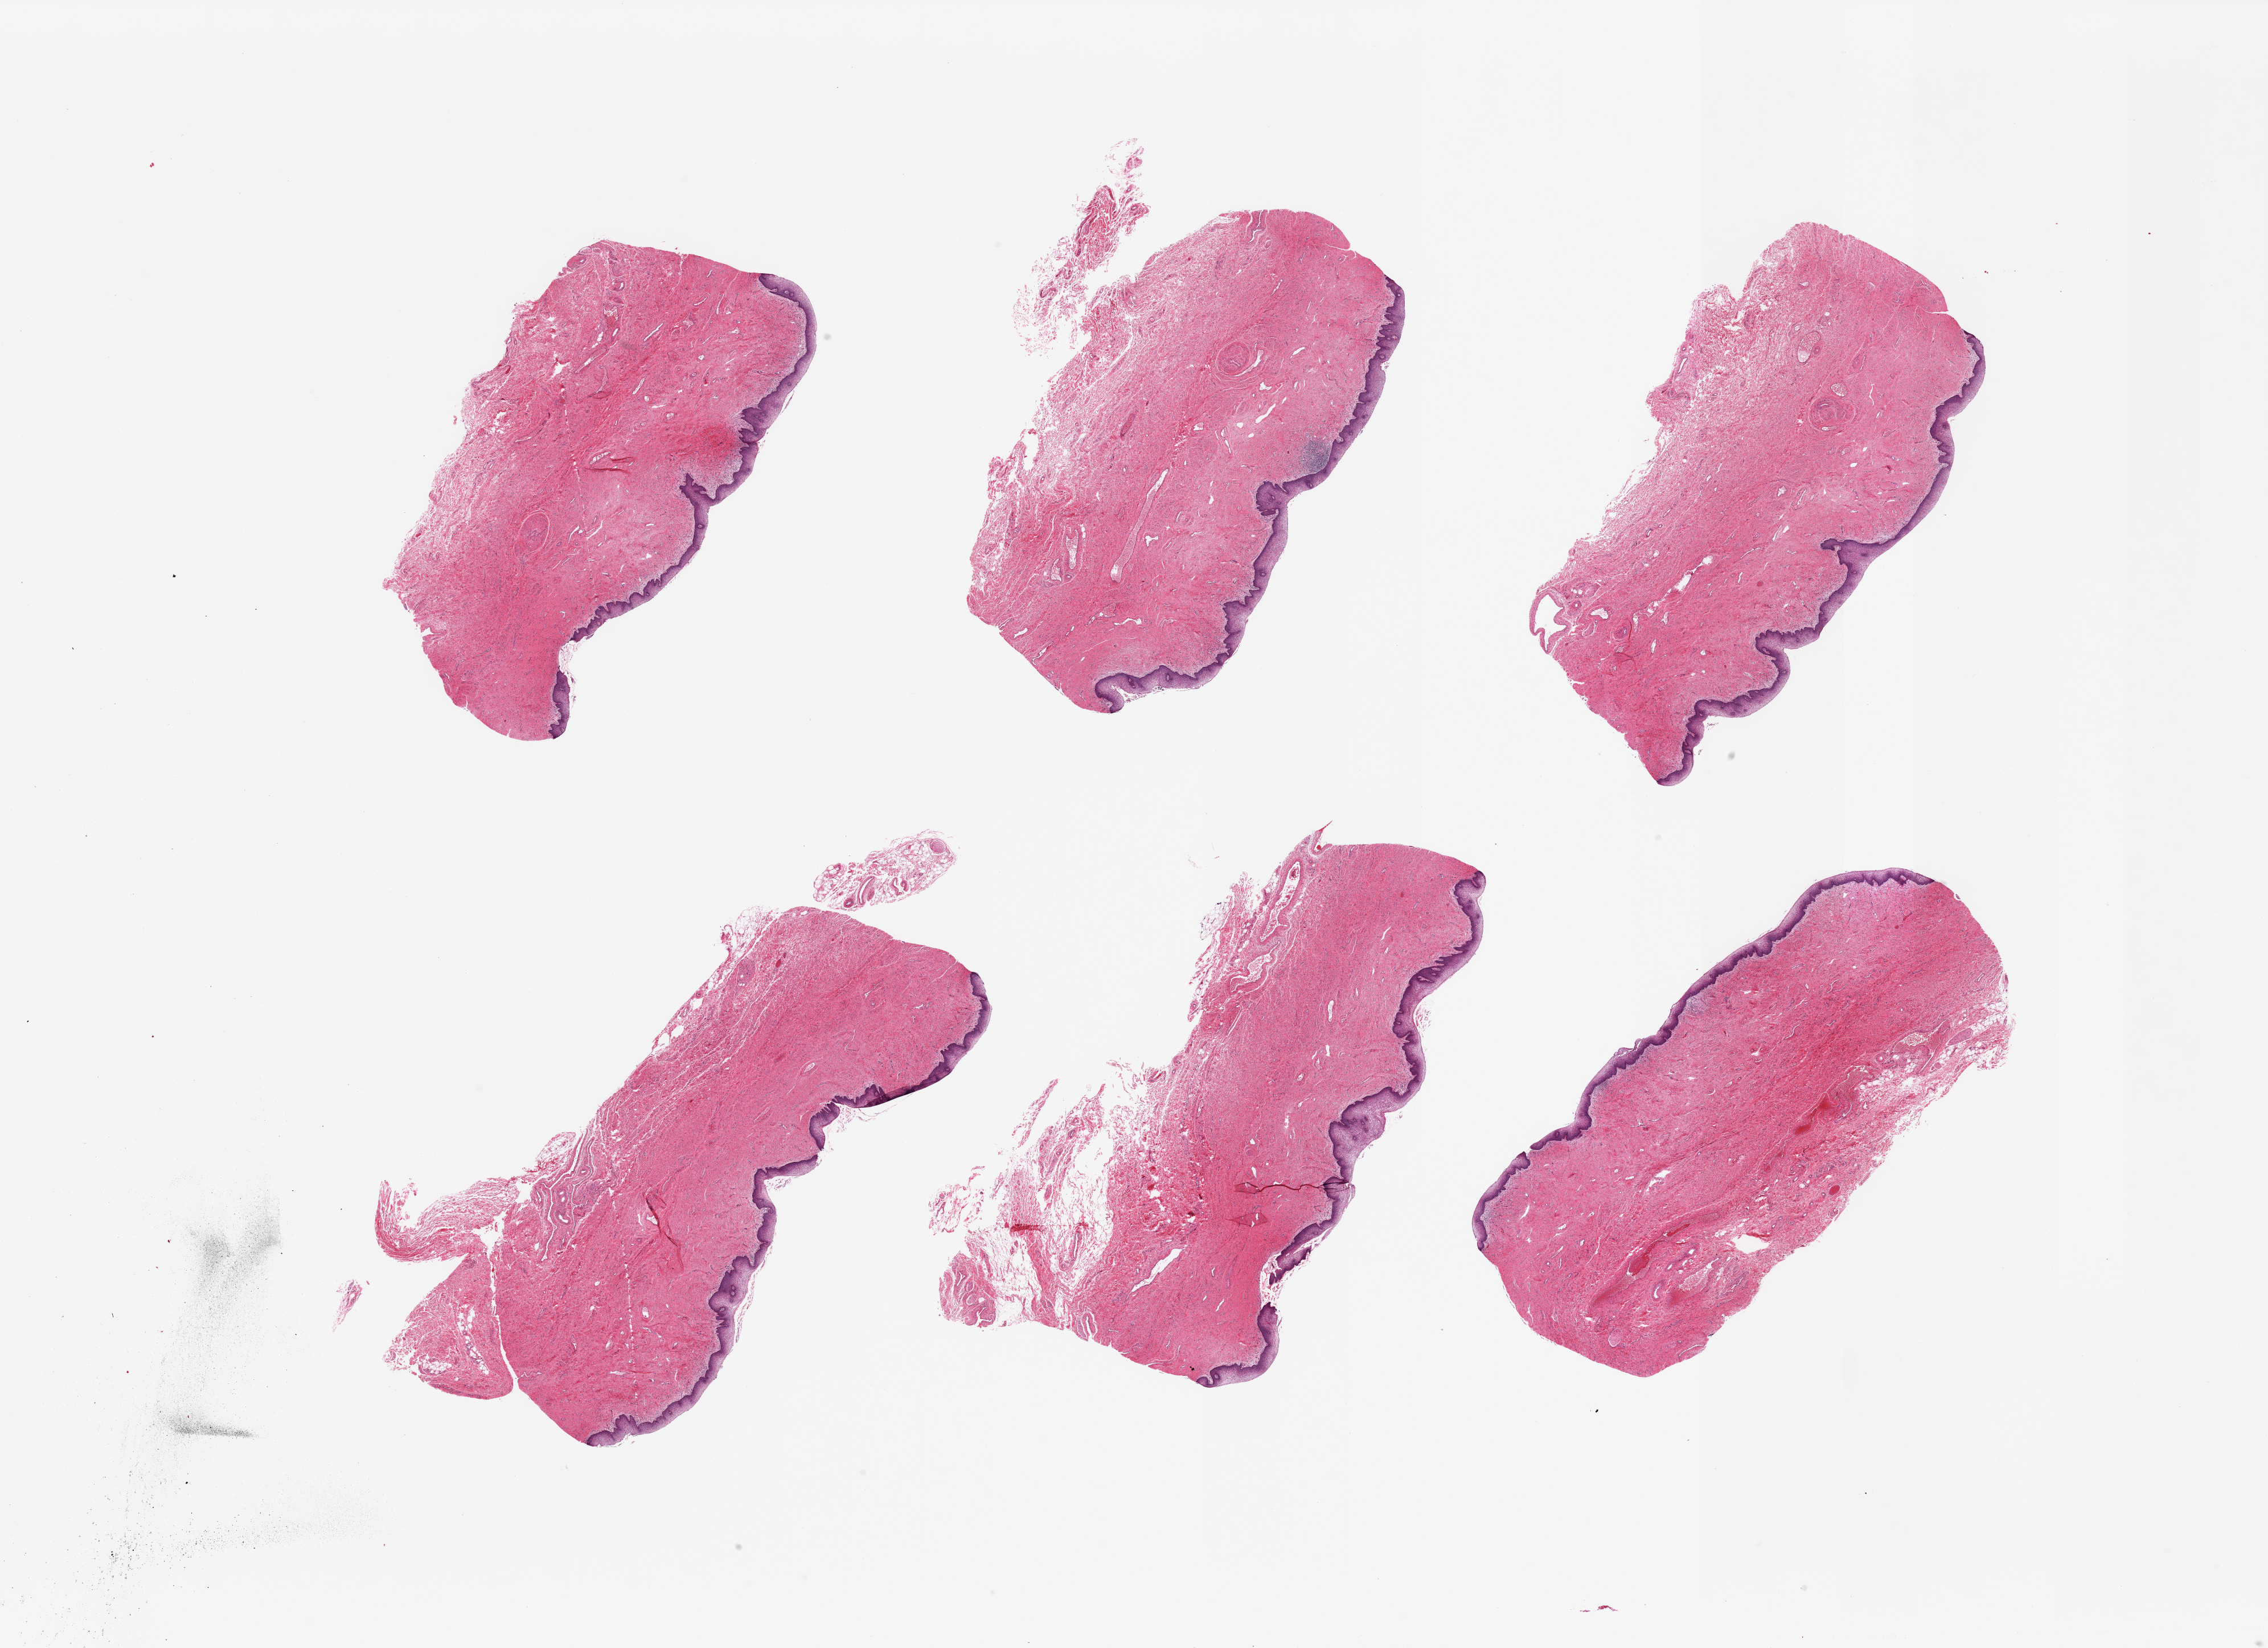
Whole-slide image, haematoxylin and eosin stain — low-resolution overview of the scanned area, about 31.5 x 22.9 mm (acquisition: 20x scan), PAXgene-fixed, paraffin-embedded tissue, section of vagina (target tissue), tissue donor sample.
Reviewer comment on this tissue sample: 6 pieces, squamous mucosa up to ~0.2mm.